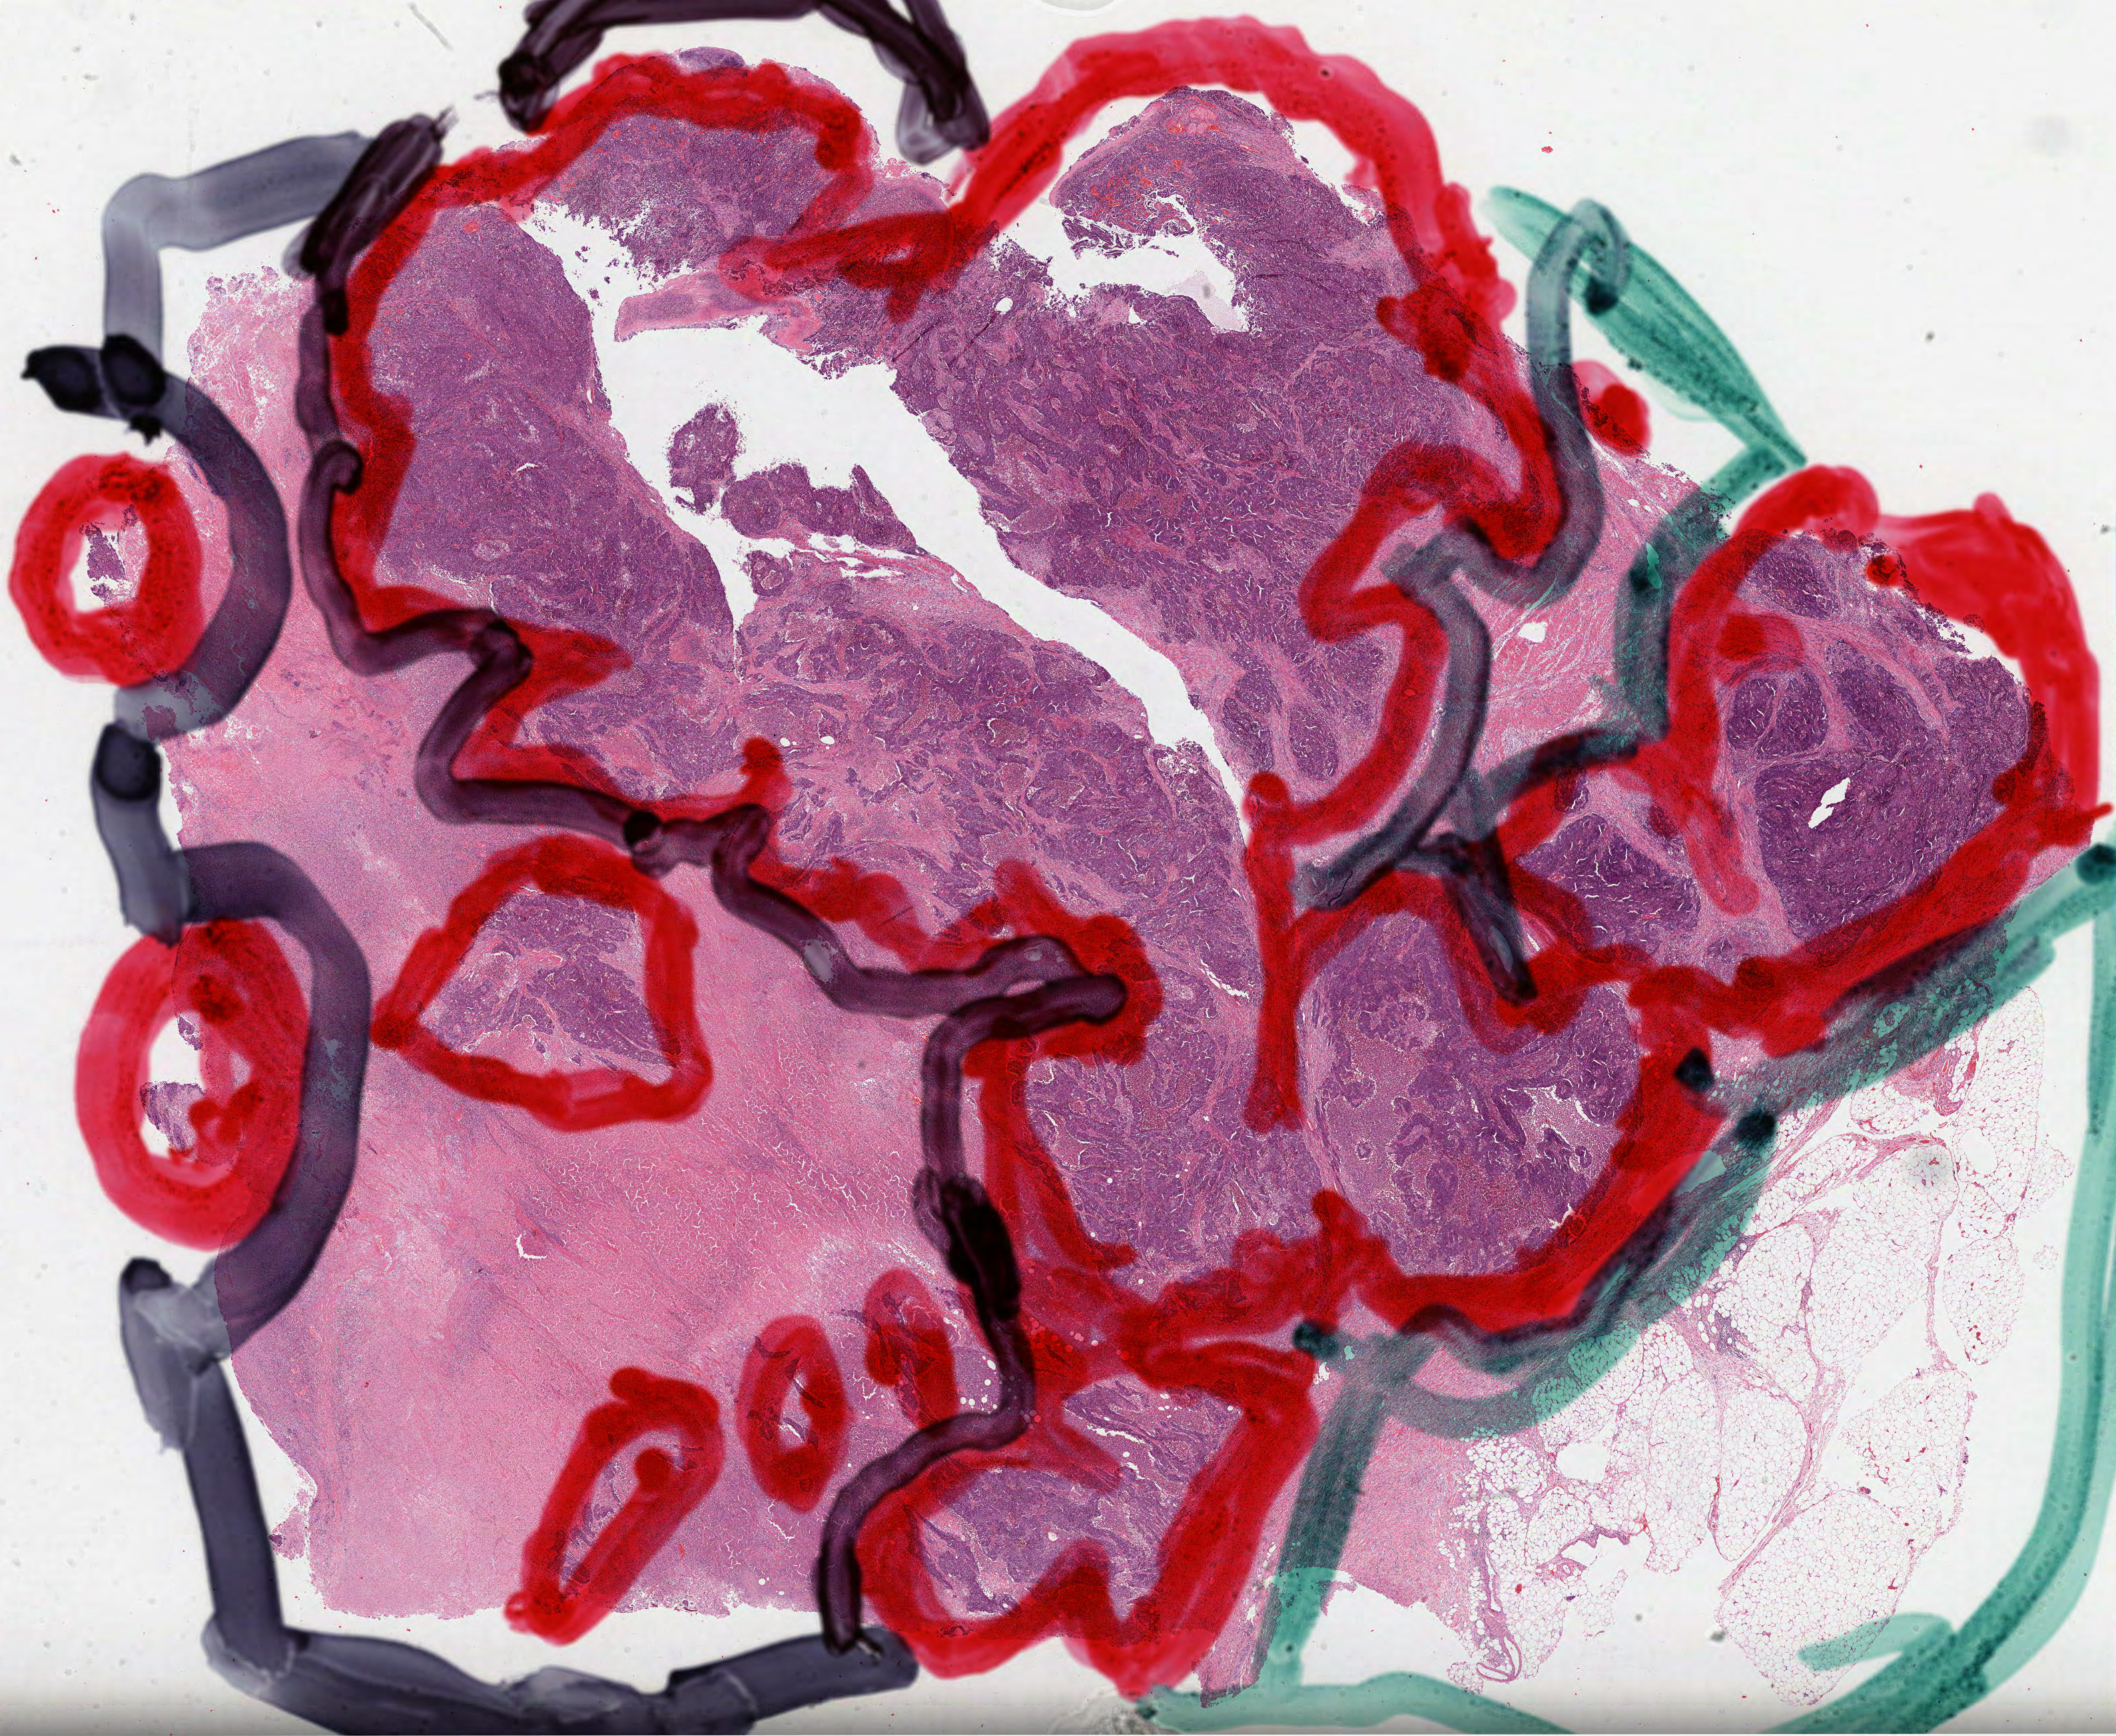
Digitized H&E-stained tissue section (whole slide) — whole scanned area (about 25.6 x 21.0 mm, slide scanned at 40x) shown as a low-resolution overview. Formalin-fixed paraffin-embedded (FFPE) diagnostic section. Primary tumour sample from the stomach. Female, age 70 years at initial diagnosis.
Diagnosis: Adenocarcinoma, NOS.